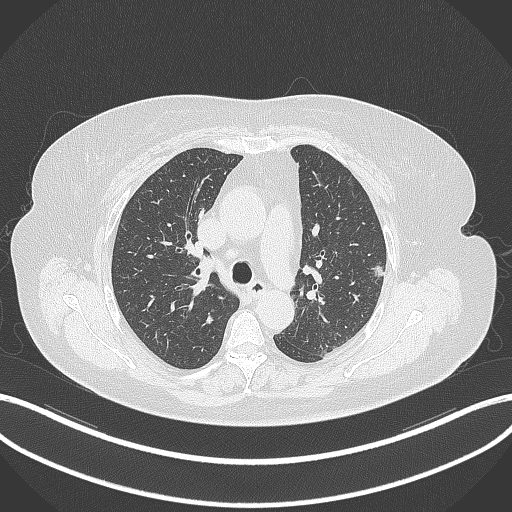
Chest CT, one axial slice; position 215 of 309 along the scan axis; lung window (W 1500 / L -600 HU); 1 mm slice thickness; 512 × 512 image matrix. Patient: female, 70 years. Case-level facts recorded for this patient, not image findings: clinical TNM (as recorded): T1c N0 M0.
Outlined on this slice (bounding box drawn by a radiologist):
- lung tumour (recorded histology: adenocarcinoma): bounding box <368,261,387,281> (left, top, right, bottom; pixels)